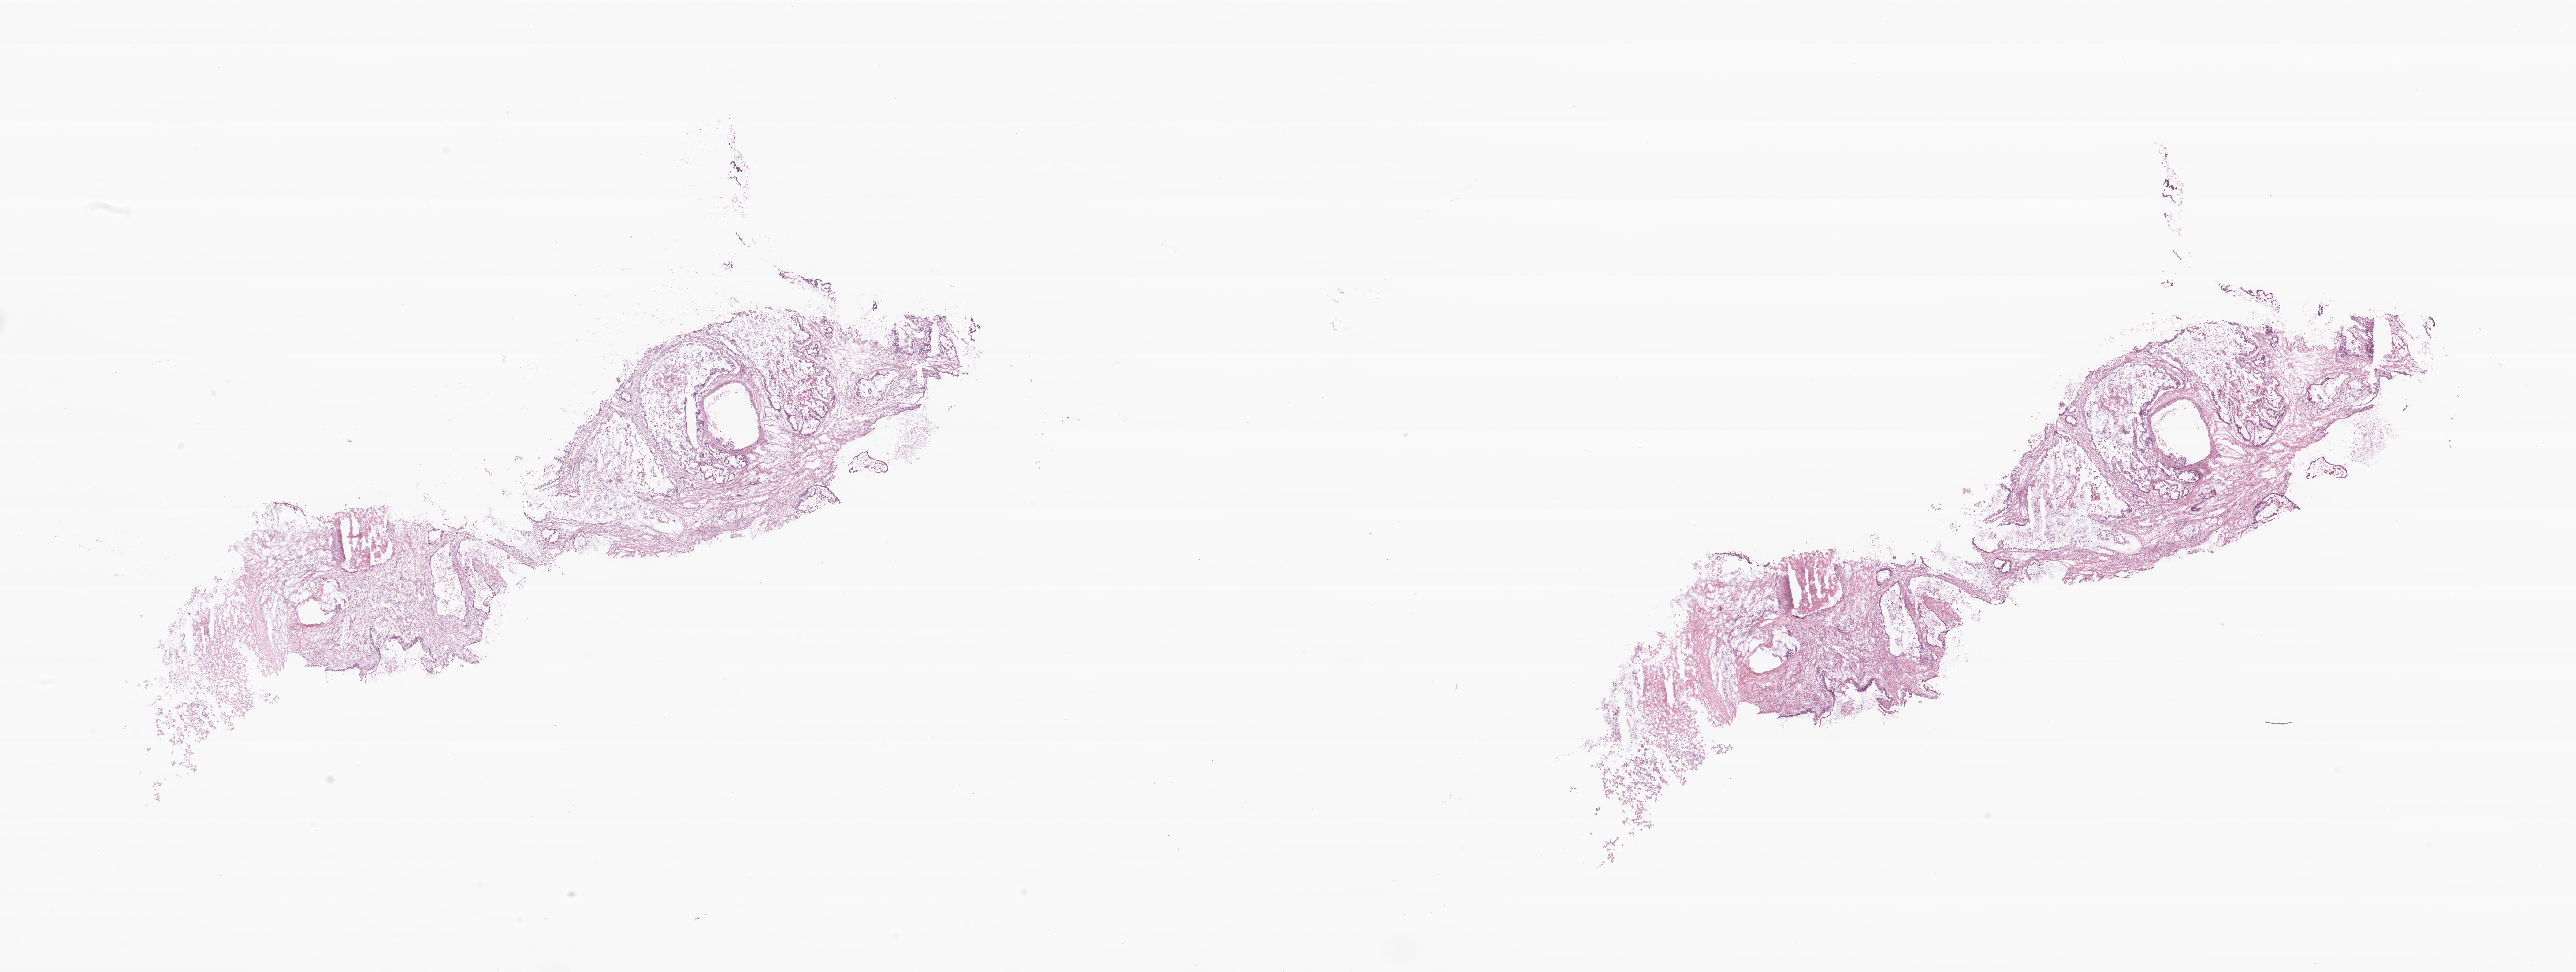
Digitized H&E-stained section of tumor tissue from the ovary — whole scanned area (about 35.4 x 13.4 mm) shown as a low-resolution overview. Frozen section. Patient: female, age 191 months.
Diagnosis (ICD-O-3 morphology term): Intraductal papillary/mucinous carcinoma, invasive.